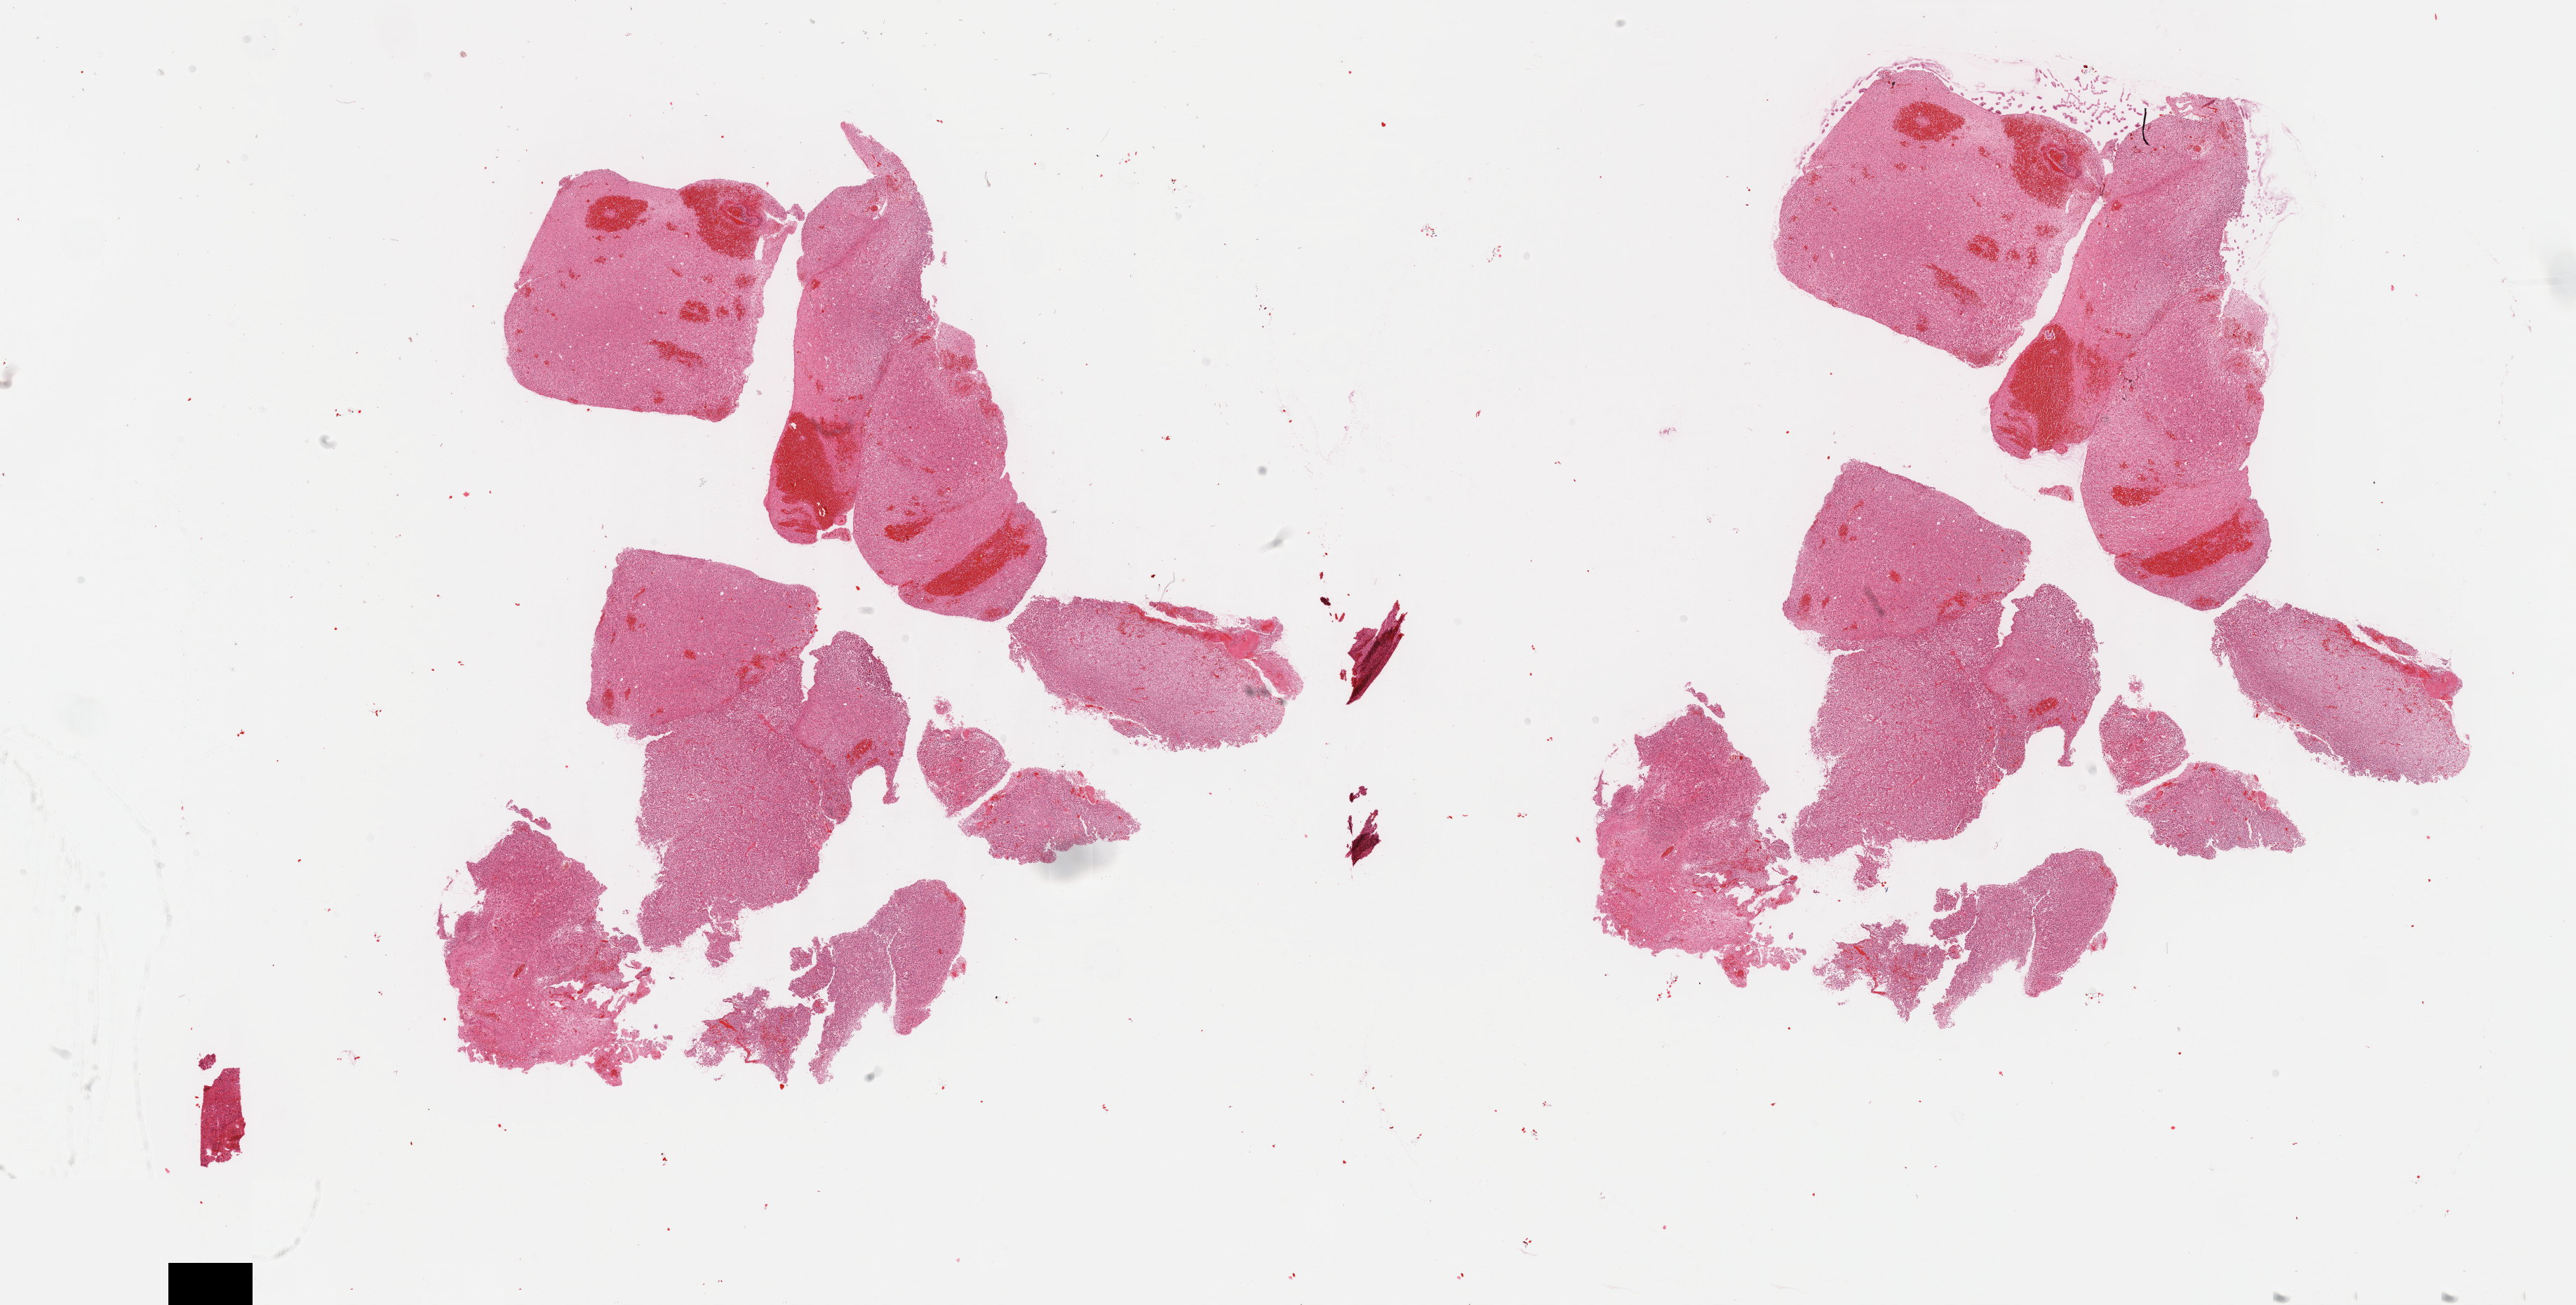
H&E whole-slide image, low-resolution overview of the scanned area, about 29.7 x 15.0 mm; formalin-fixed paraffin-embedded (FFPE) diagnostic section; primary tumour sample from the brain. Patient: male, age at initial diagnosis 39 years. Histologic grade: G3 (poorly differentiated).
Pathologic diagnosis: Mixed glioma (cerebrum).